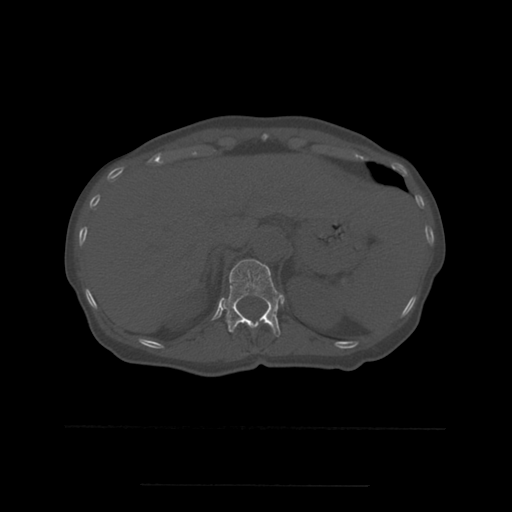
CT including the spine, one axial slice. Position 262 of 544 along the scan axis. Bone window (W 1800 / L 400 HU). 512 × 512 image matrix. Patient age 58 years. From the clinical record (not read from this slice): primary cancer: lung.
Annotated regions visible in this slice (semi-automatic segmentation, software-assisted and operator-edited):
- T12 vertebra: box from (x=224, y=259) to (x=284, y=337) px